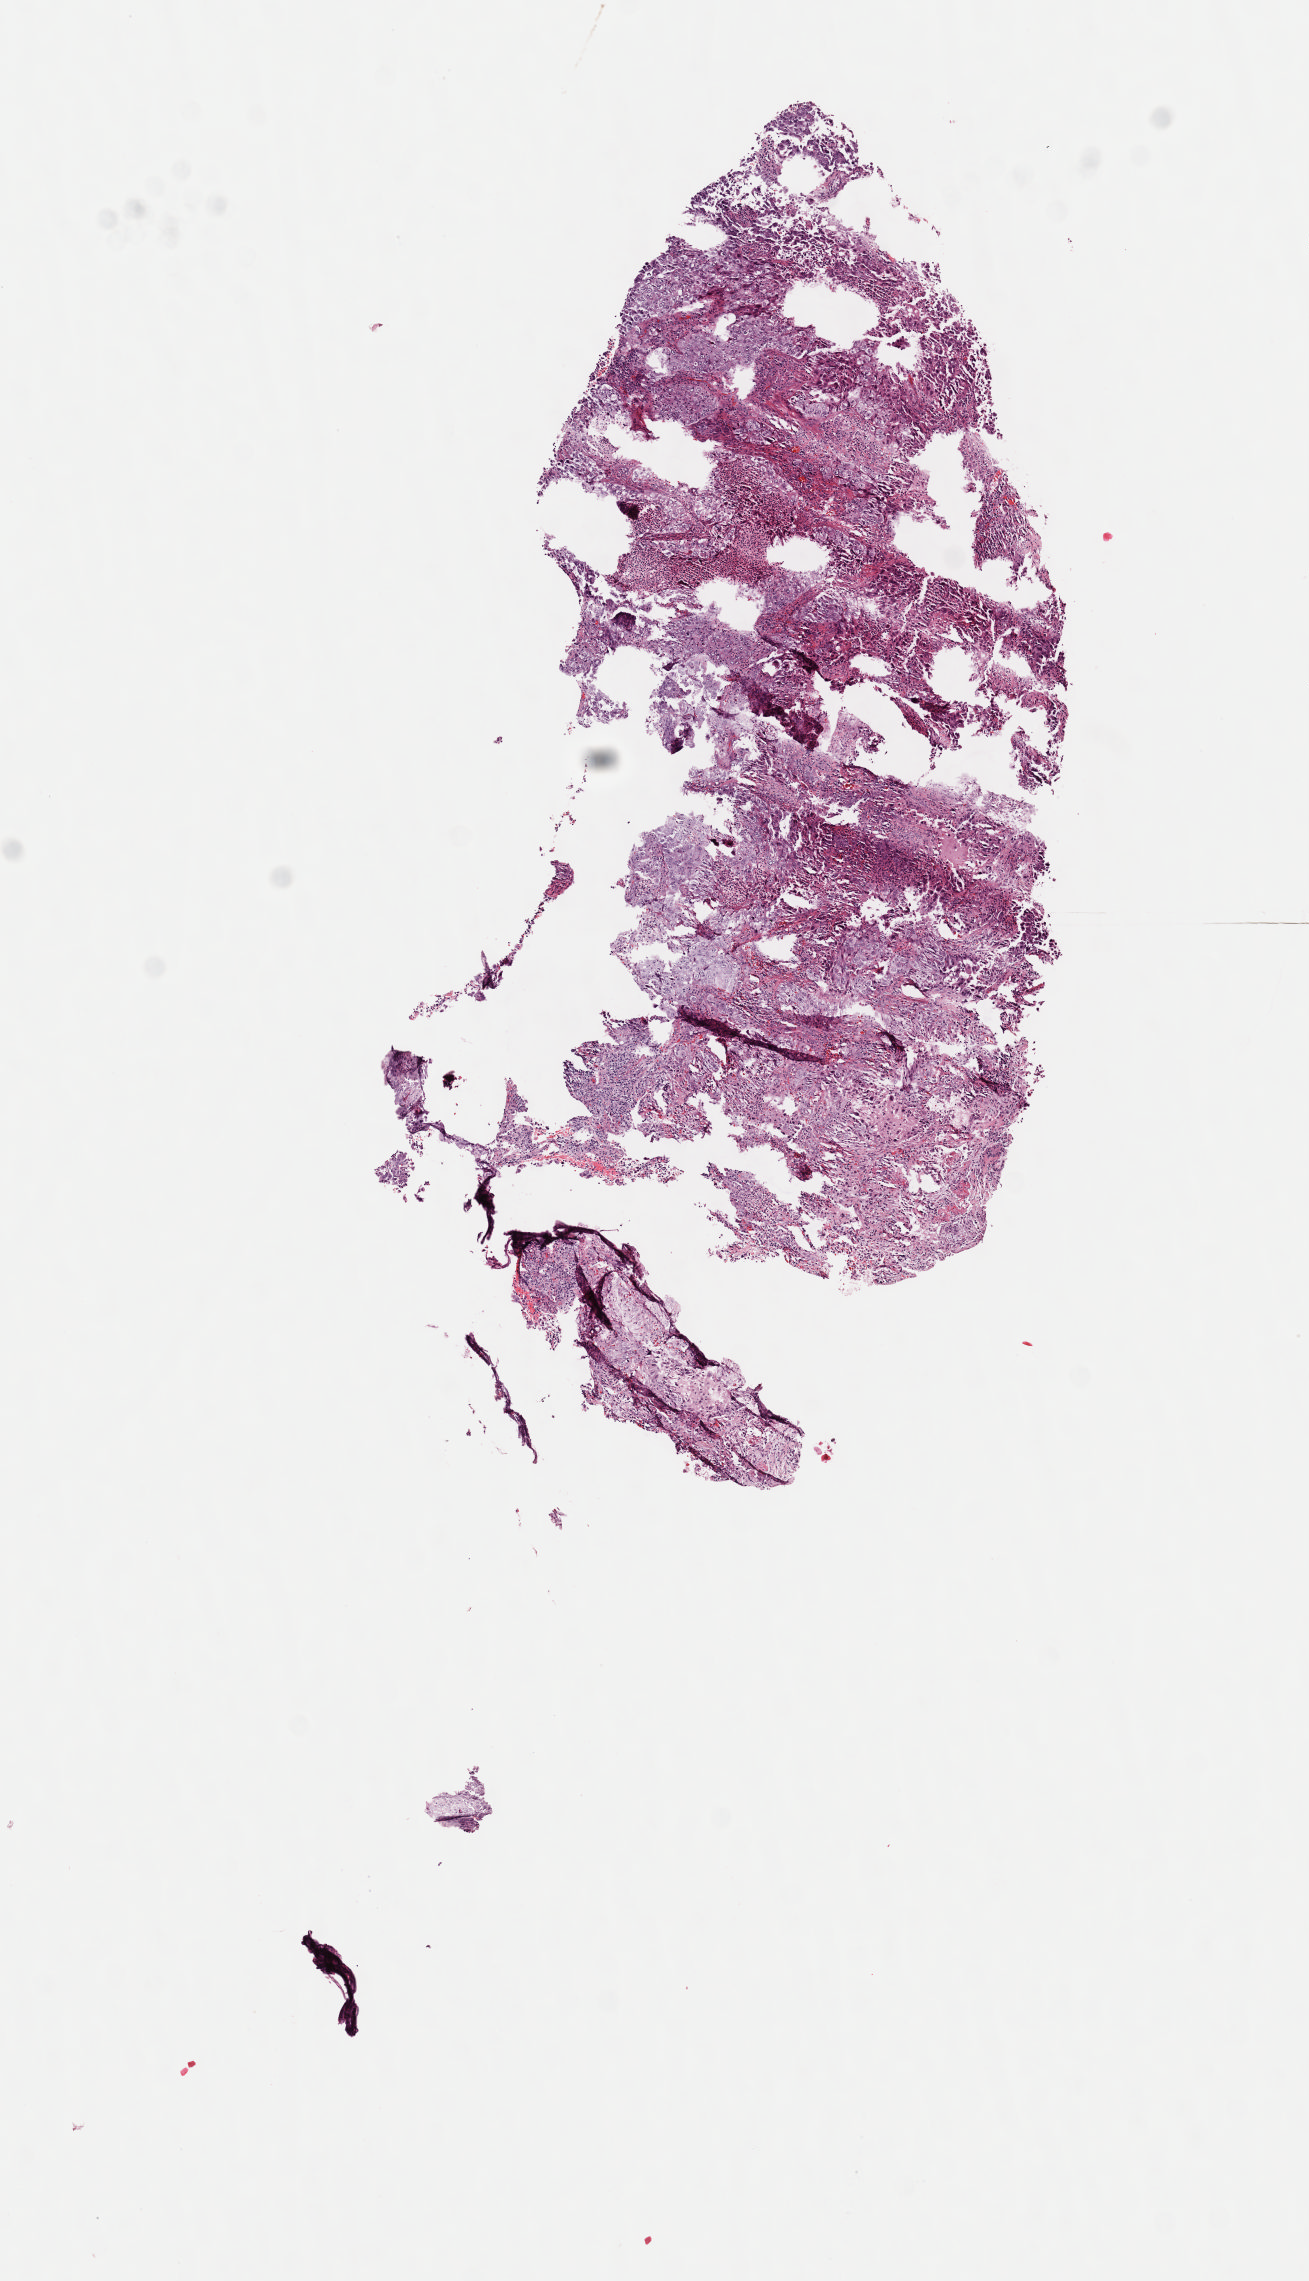
Digitized Hematoxylin and eosin (H&E) stained tissue section (whole slide), shown as a low-resolution overview of the whole scanned area (about 5.2 x 9.0 mm, acquisition: 40x scan); frozen section; sample: primary tumour, lung. Male, age 51 years at initial diagnosis. Pathologist review of this section (percent, as recorded): tumour cells 50%, tumour nuclei 60%, normal cells 0%, stromal cells 30%, necrosis 20%. Inflammatory infiltration, as recorded: lymphocyte infiltration 50%, monocyte infiltration 20%, neutrophil infiltration 30%.
AJCC pathologic stage: IB. Pathologic diagnosis: Adenocarcinoma, NOS. TNM: T2 N0 M0.